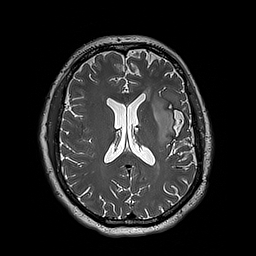
Brain MRI from a brain-tumour surgery series, one axial slice; slice 90 of 192 in the series (ordered by position); 1 mm slice thickness; 256 × 256 image matrix, field of view 250 × 250 mm. Case-level facts recorded for this patient, not image findings: histopathology: Astrocytoma; WHO grade: 3; IDH mutation: yes; tumour location: Left Insular.
Annotated regions visible in this slice (expert manual segmentation):
- tumour: bounding box [x1, y1, x2, y2] px = [152, 95, 179, 145]